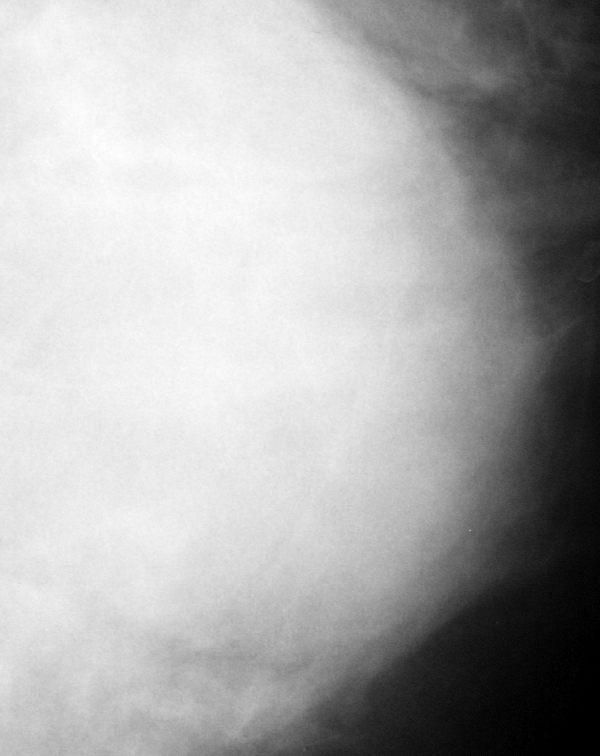
Region of interest cut from a scanned film mammogram (one marked finding), left breast, CC view.
Finding: mass, shape round, margins obscured; BI-RADS assessment category 4; subtlety rating 5 on a 1 (subtle) to 5 (obvious) scale; pathology result (as recorded, not read from the image): benign.